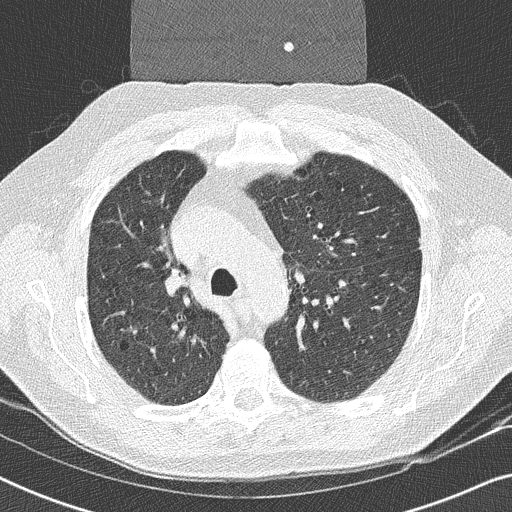
Low-dose screening chest CT, axial slice, second screening round (one year after baseline), lung window (W 1500 / L -600 HU), slice 82 of 252 in the series, 512 × 512 image matrix, field of view 330 × 330 mm. Male participant, aged 59 years at enrolment.
- Expert-annotated lung lesion, bounding box <139,255,201,308> (left, top, right, bottom; pixels).
- The exam's reader record, not a measurement of the box and not confirmed to be the same lesion: non-calcified nodule or mass ≥4 mm, right upper lobe, 17 × 16 mm, smooth margins, soft tissue attenuation, pre-existing on the prior screen: yes.
- Official screen result: positive, other.